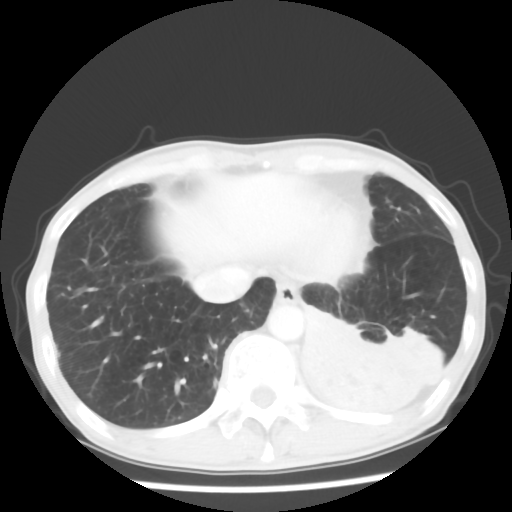
Chest CT, one axial slice. Position 12 of 64 along the scan axis. Reconstruction kernel STANDARD. 120 kVp. Lung window (W 1500 / L -600 HU). 5 mm slice thickness. 512 × 512 image matrix, field of view 313 × 313 mm. Male patient, age 68 years. Case-level facts recorded for this patient, not image findings: clinical TNM (as recorded): T4 N0 M0.
Outlined on this slice (bounding box drawn by a radiologist):
- lung tumour (recorded histology: squamous cell carcinoma): bounding box [x1, y1, x2, y2] px = [292, 295, 459, 424]